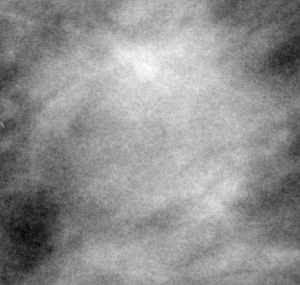
Crop from a digitized film mammogram around one marked abnormality, right breast, MLO view, BI-RADS breast density category 3 (scale 1–4).
- Marked abnormality: mass, shape irregular, margins obscured / ill defined; BI-RADS assessment category 3; subtlety rating 2 on a 1 (subtle) to 5 (obvious) scale; pathology (as recorded): malignant.